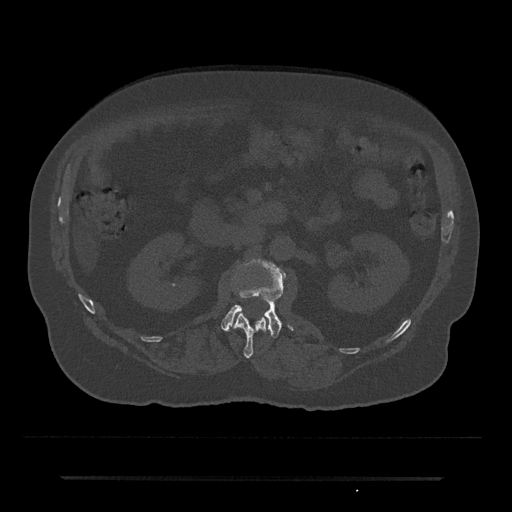
CT including the spine, one axial slice; slice 36 of 797 in the series (ordered by position); bone window (W 1800 / L 400 HU); 512 × 512 image matrix, field of view 437 × 437 mm. Male patient, age 69 years. Case-level facts recorded for this patient, not image findings: primary cancer: prostate.
Outlined on this slice (semi-automatic segmentation, software-assisted and operator-edited):
- L1 vertebra: bounding box (x1, y1, x2, y2) in pixels: (233, 313, 267, 358)
- L2 vertebra: (221, 260, 293, 338)